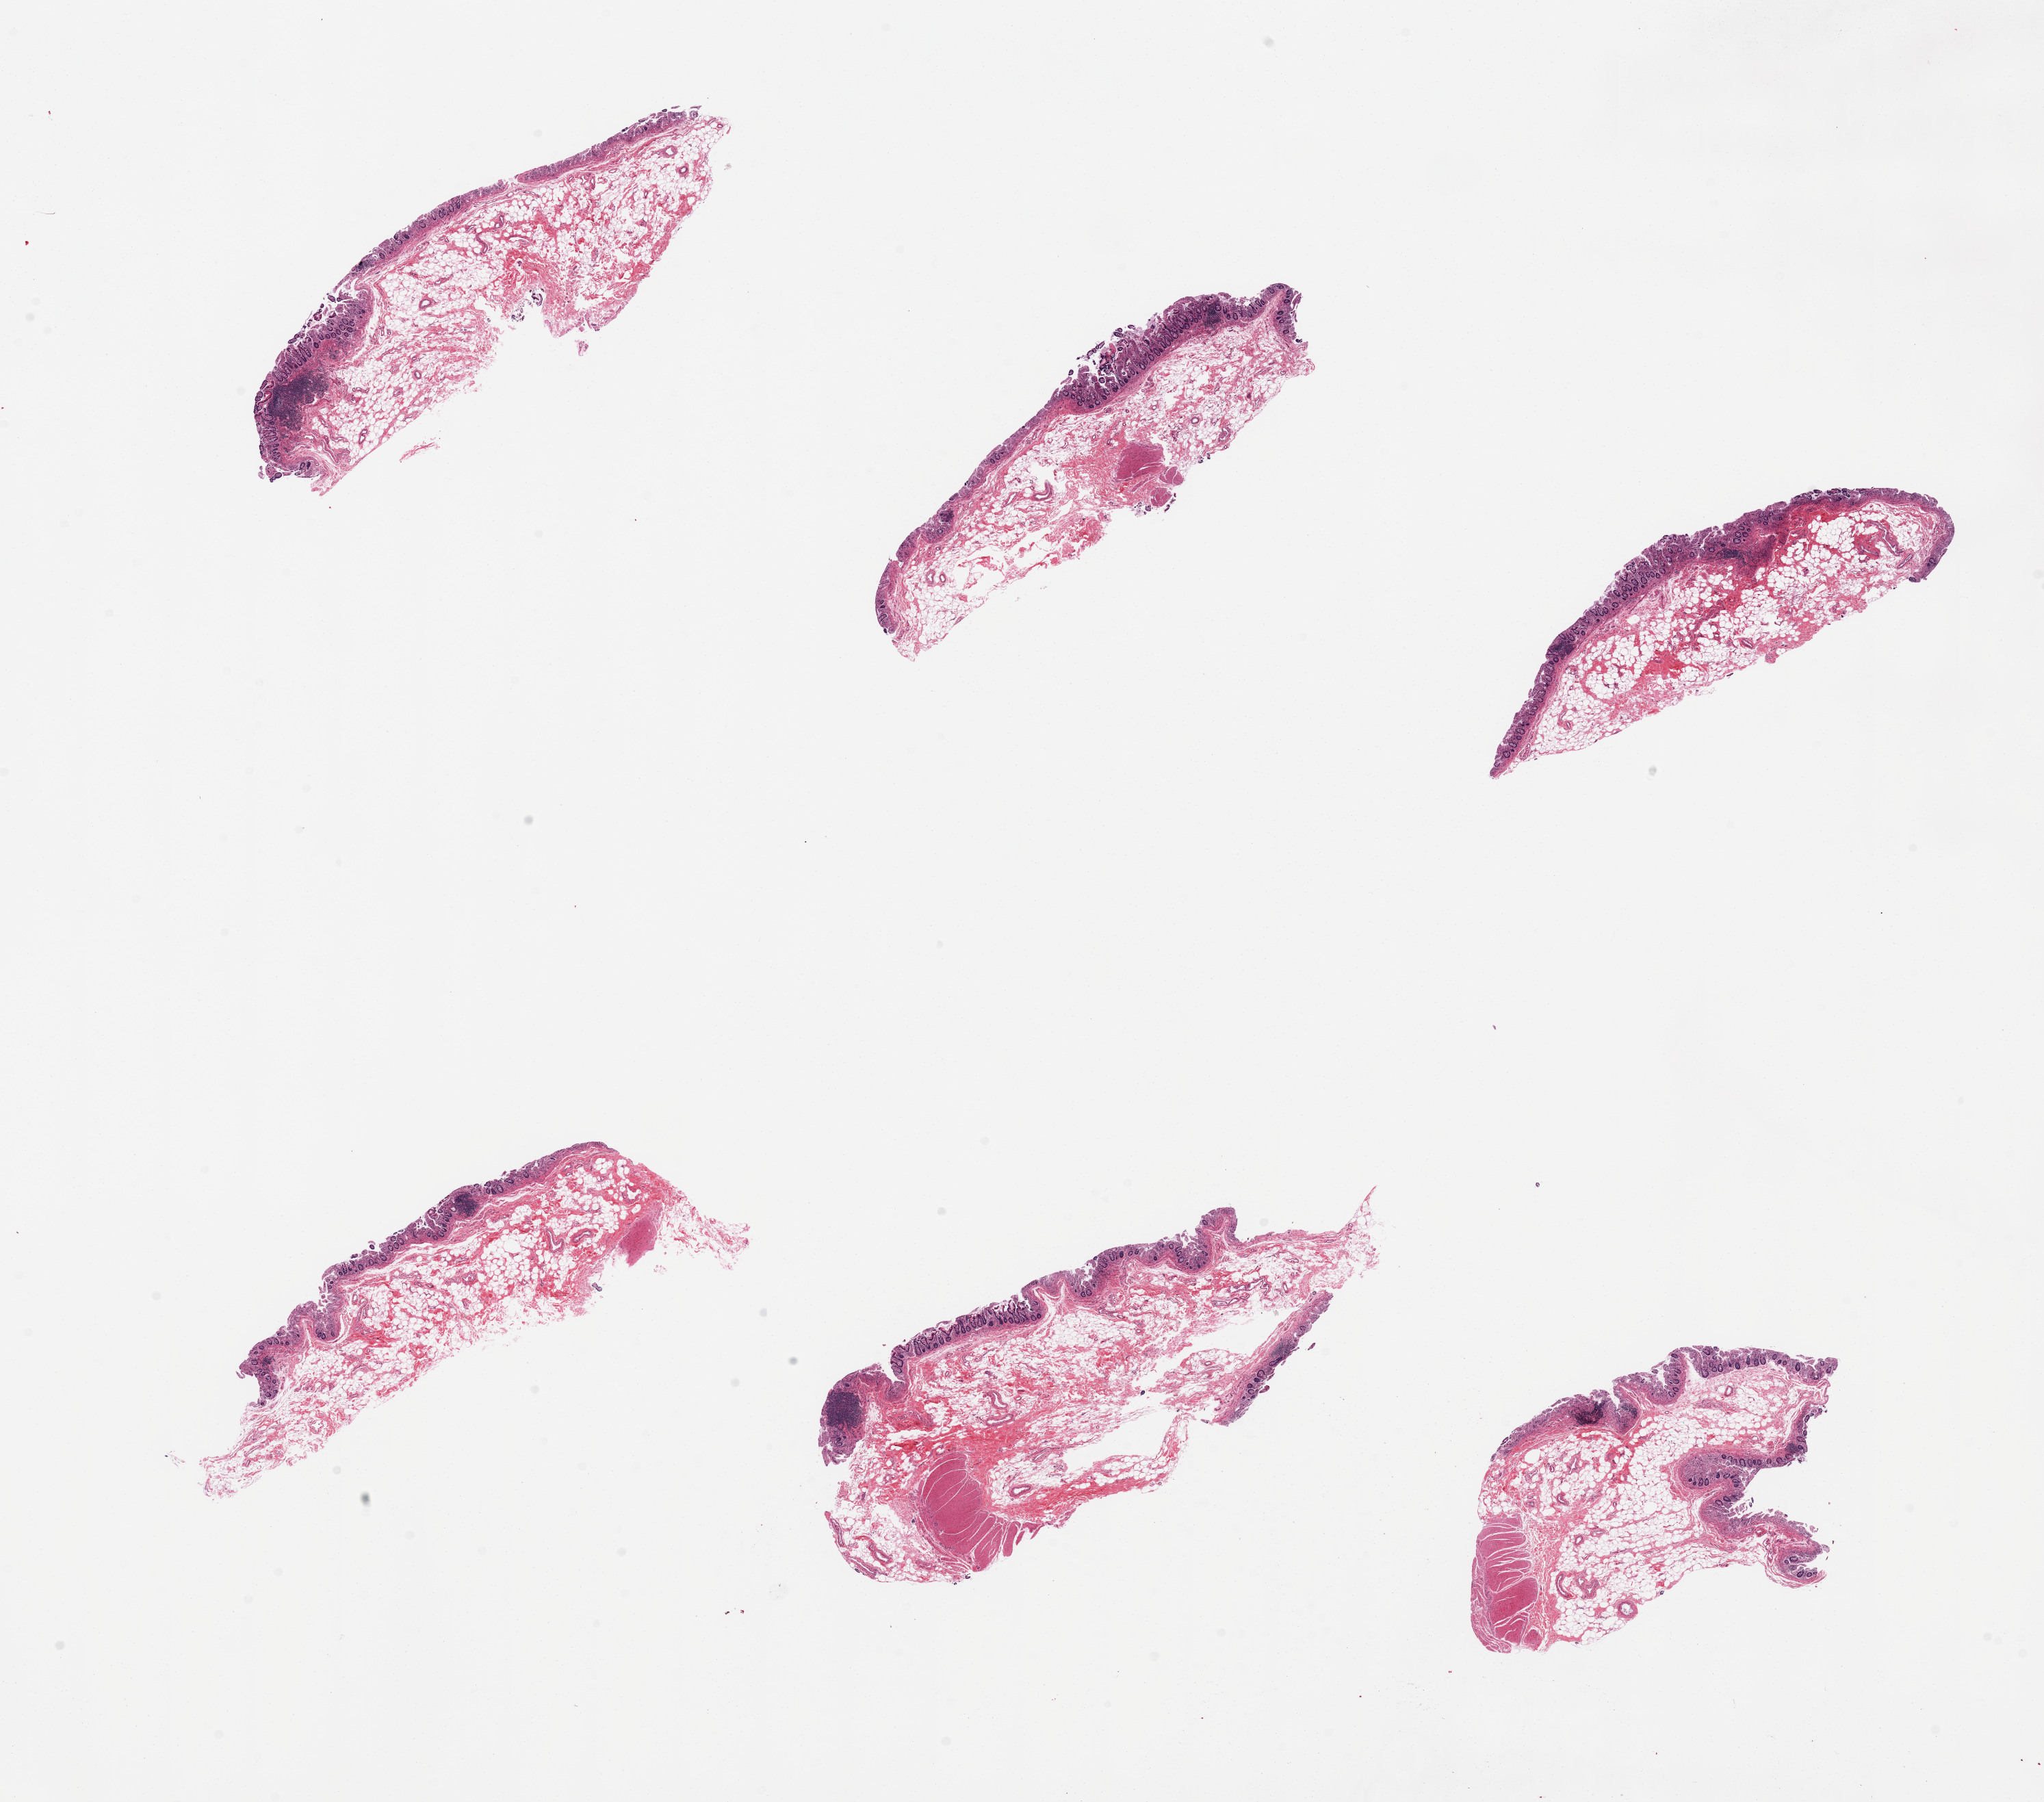
Digitized haematoxylin and eosin-stained section, a low-resolution overview of the entire scanned area, about 23.6 x 20.8 mm (from a 20x scan), PAXgene-fixed paraffin-embedded (PFPE) section, target tissue: ileum, donor tissue sample. Female donor.
Pathologist's review note for this sample: 6 pieces, mucosa moderately autolyzed but lymphoid aggregates well preserved, ~5-10% of sections.